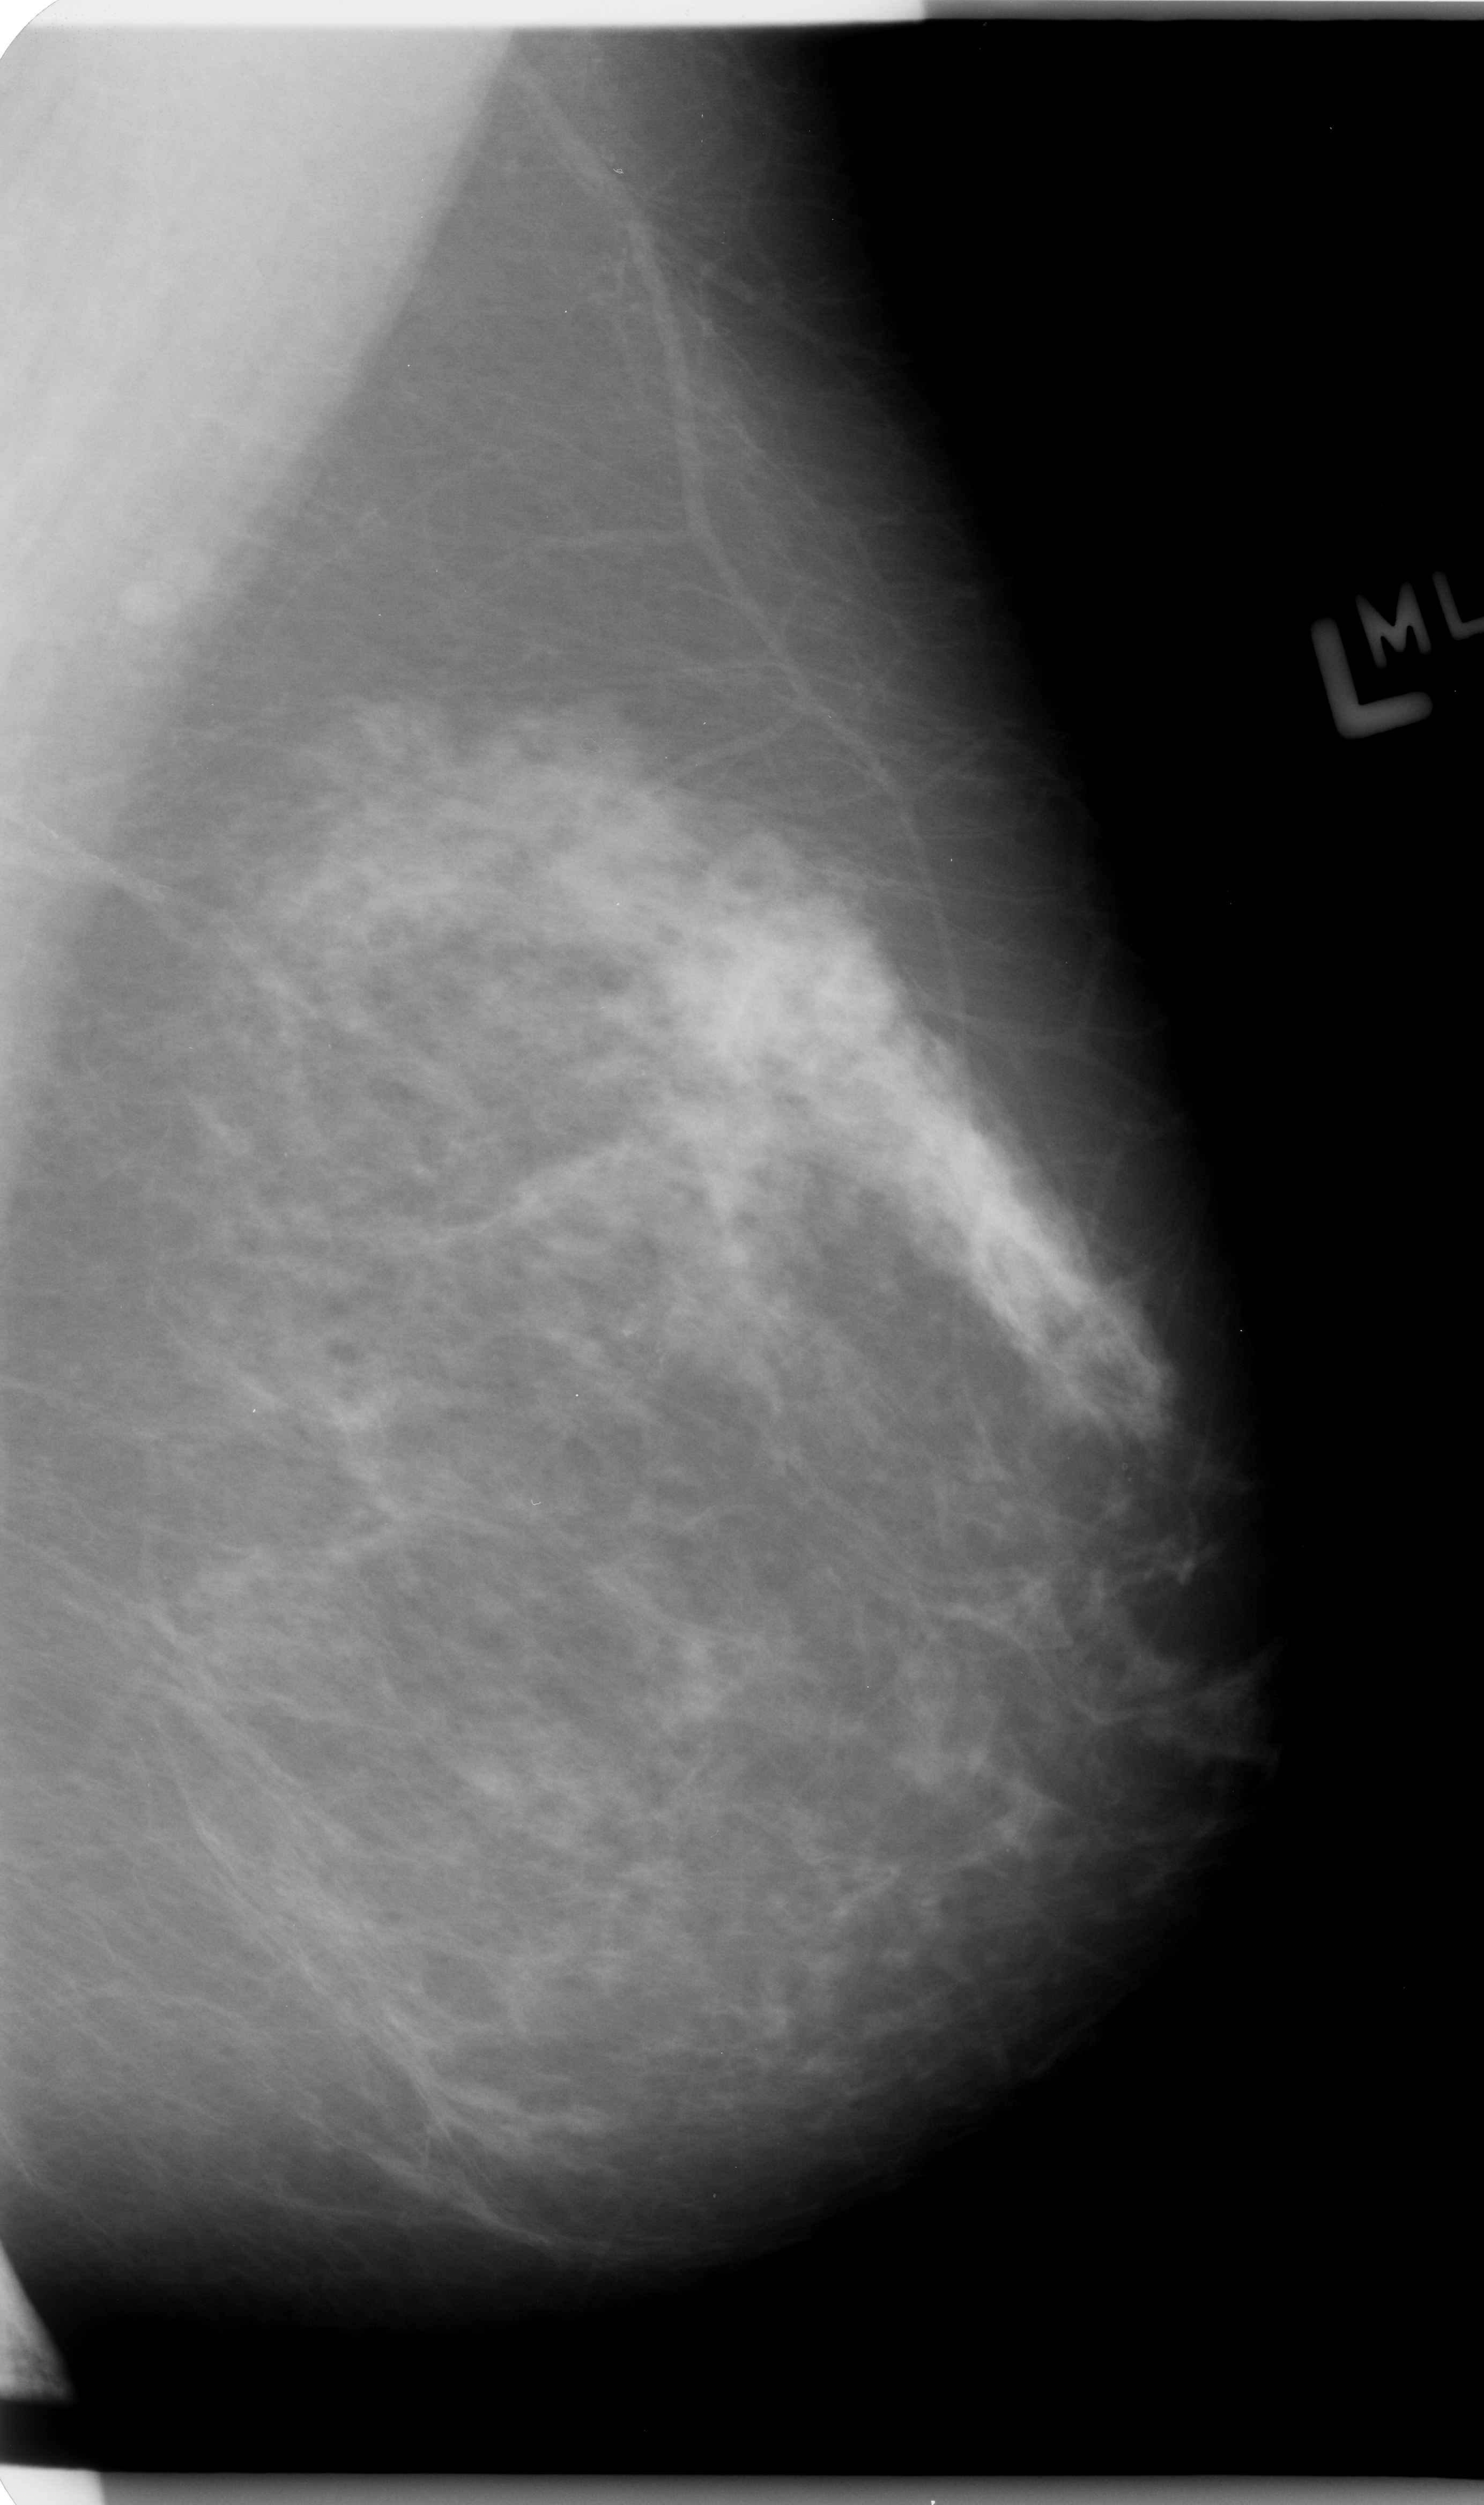
Mammogram (digitized film), left breast, mediolateral oblique (MLO) view.
Radiologist-marked abnormalities on this image: calcifications, morphology pleomorphic, distribution clustered; BI-RADS assessment category 4; subtlety rating 3 on a 1 (subtle) to 5 (obvious) scale; pathology result (as recorded, not read from the image): benign.